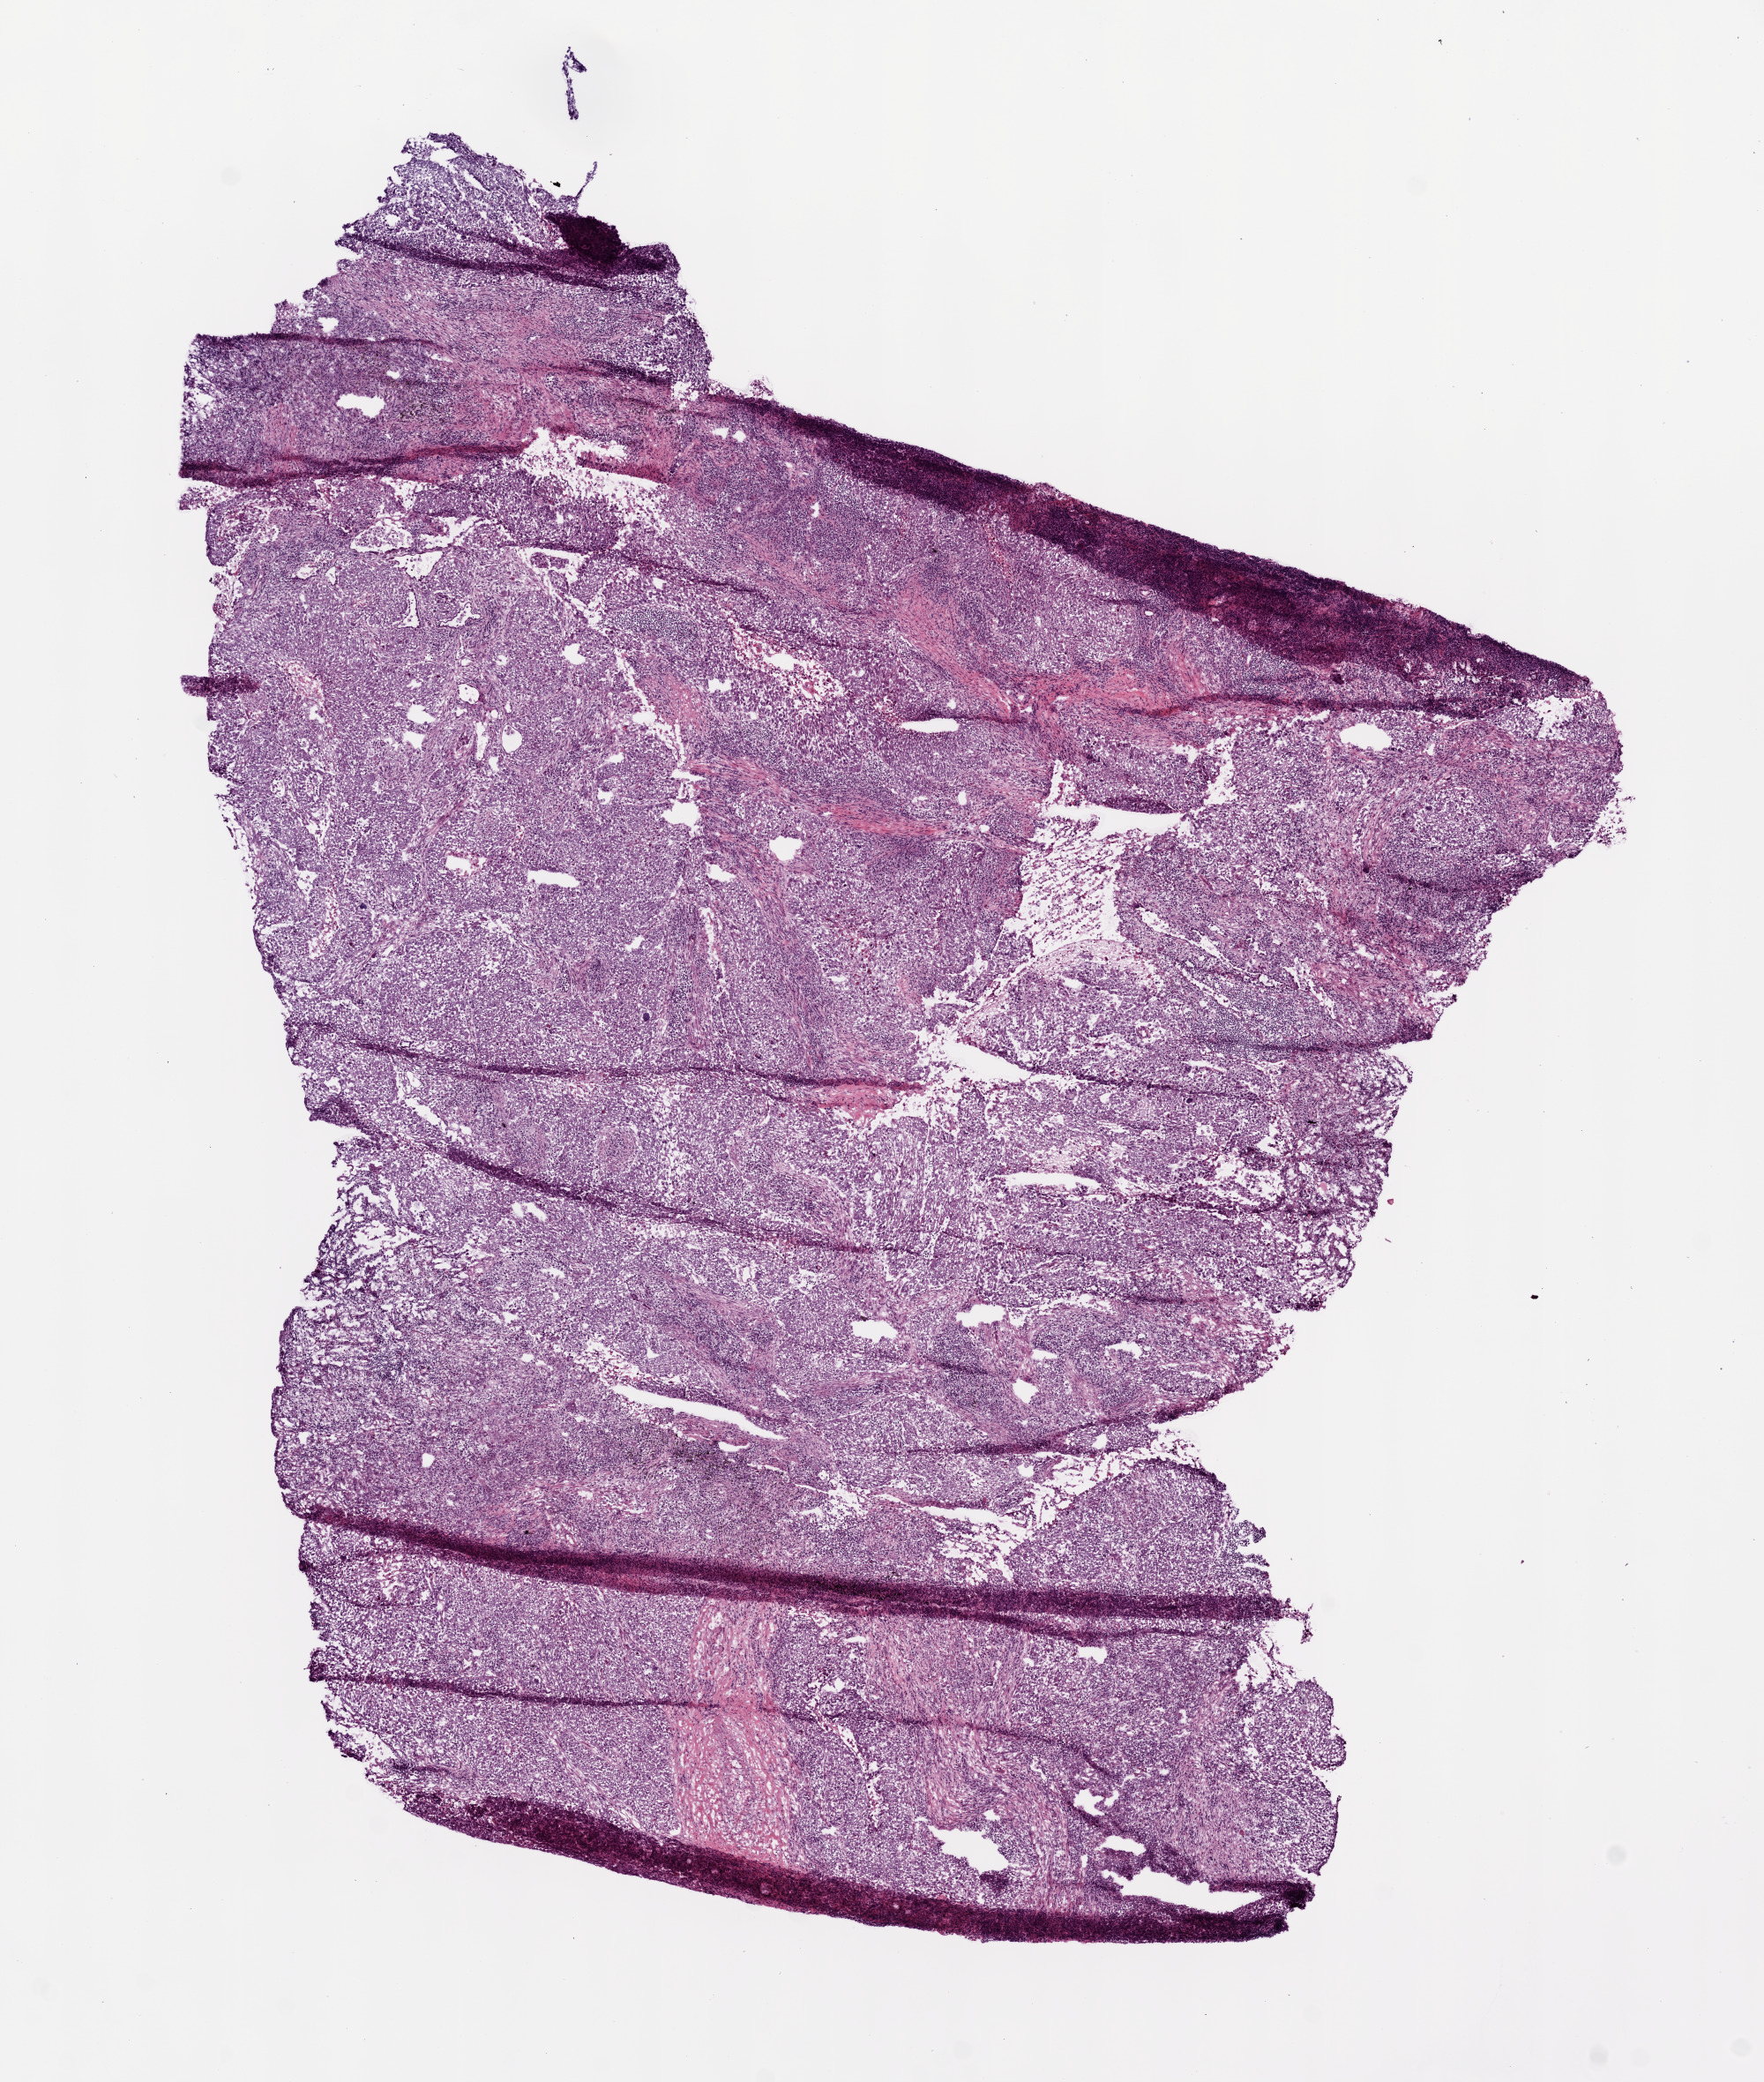
Digitized H&E tissue section (whole slide), low-resolution overview of the scanned area, about 8.0 x 9.5 mm; frozen section; sample: primary tumour, lung. Male, age 74 years at initial diagnosis. Slide review estimates, as recorded: tumour cells 80%, tumour nuclei 75%, normal cells 0%, stromal cells 15%, necrosis 5%.
Diagnosis: Squamous cell carcinoma, NOS. AJCC pathologic stage: IA.